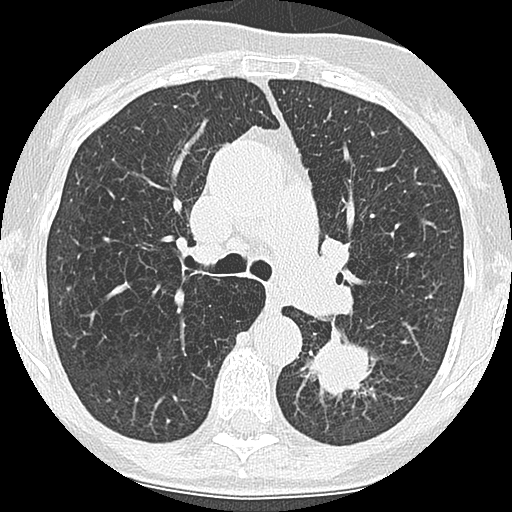
Low-dose screening chest CT, one axial slice; slice 113 of 171 in the series (ordered by position); reconstruction kernel LUNG; 120 kVp; lung window (W 1500 / L -600 HU); 2.5 mm slice thickness; 512 × 512 image matrix, field of view 280 × 280 mm.
Outlined on this slice (outlined manually by an expert reader):
- lesion 1 (tumor, lower lobe of left lung): bounding box <309,340,369,395> (left, top, right, bottom; pixels)